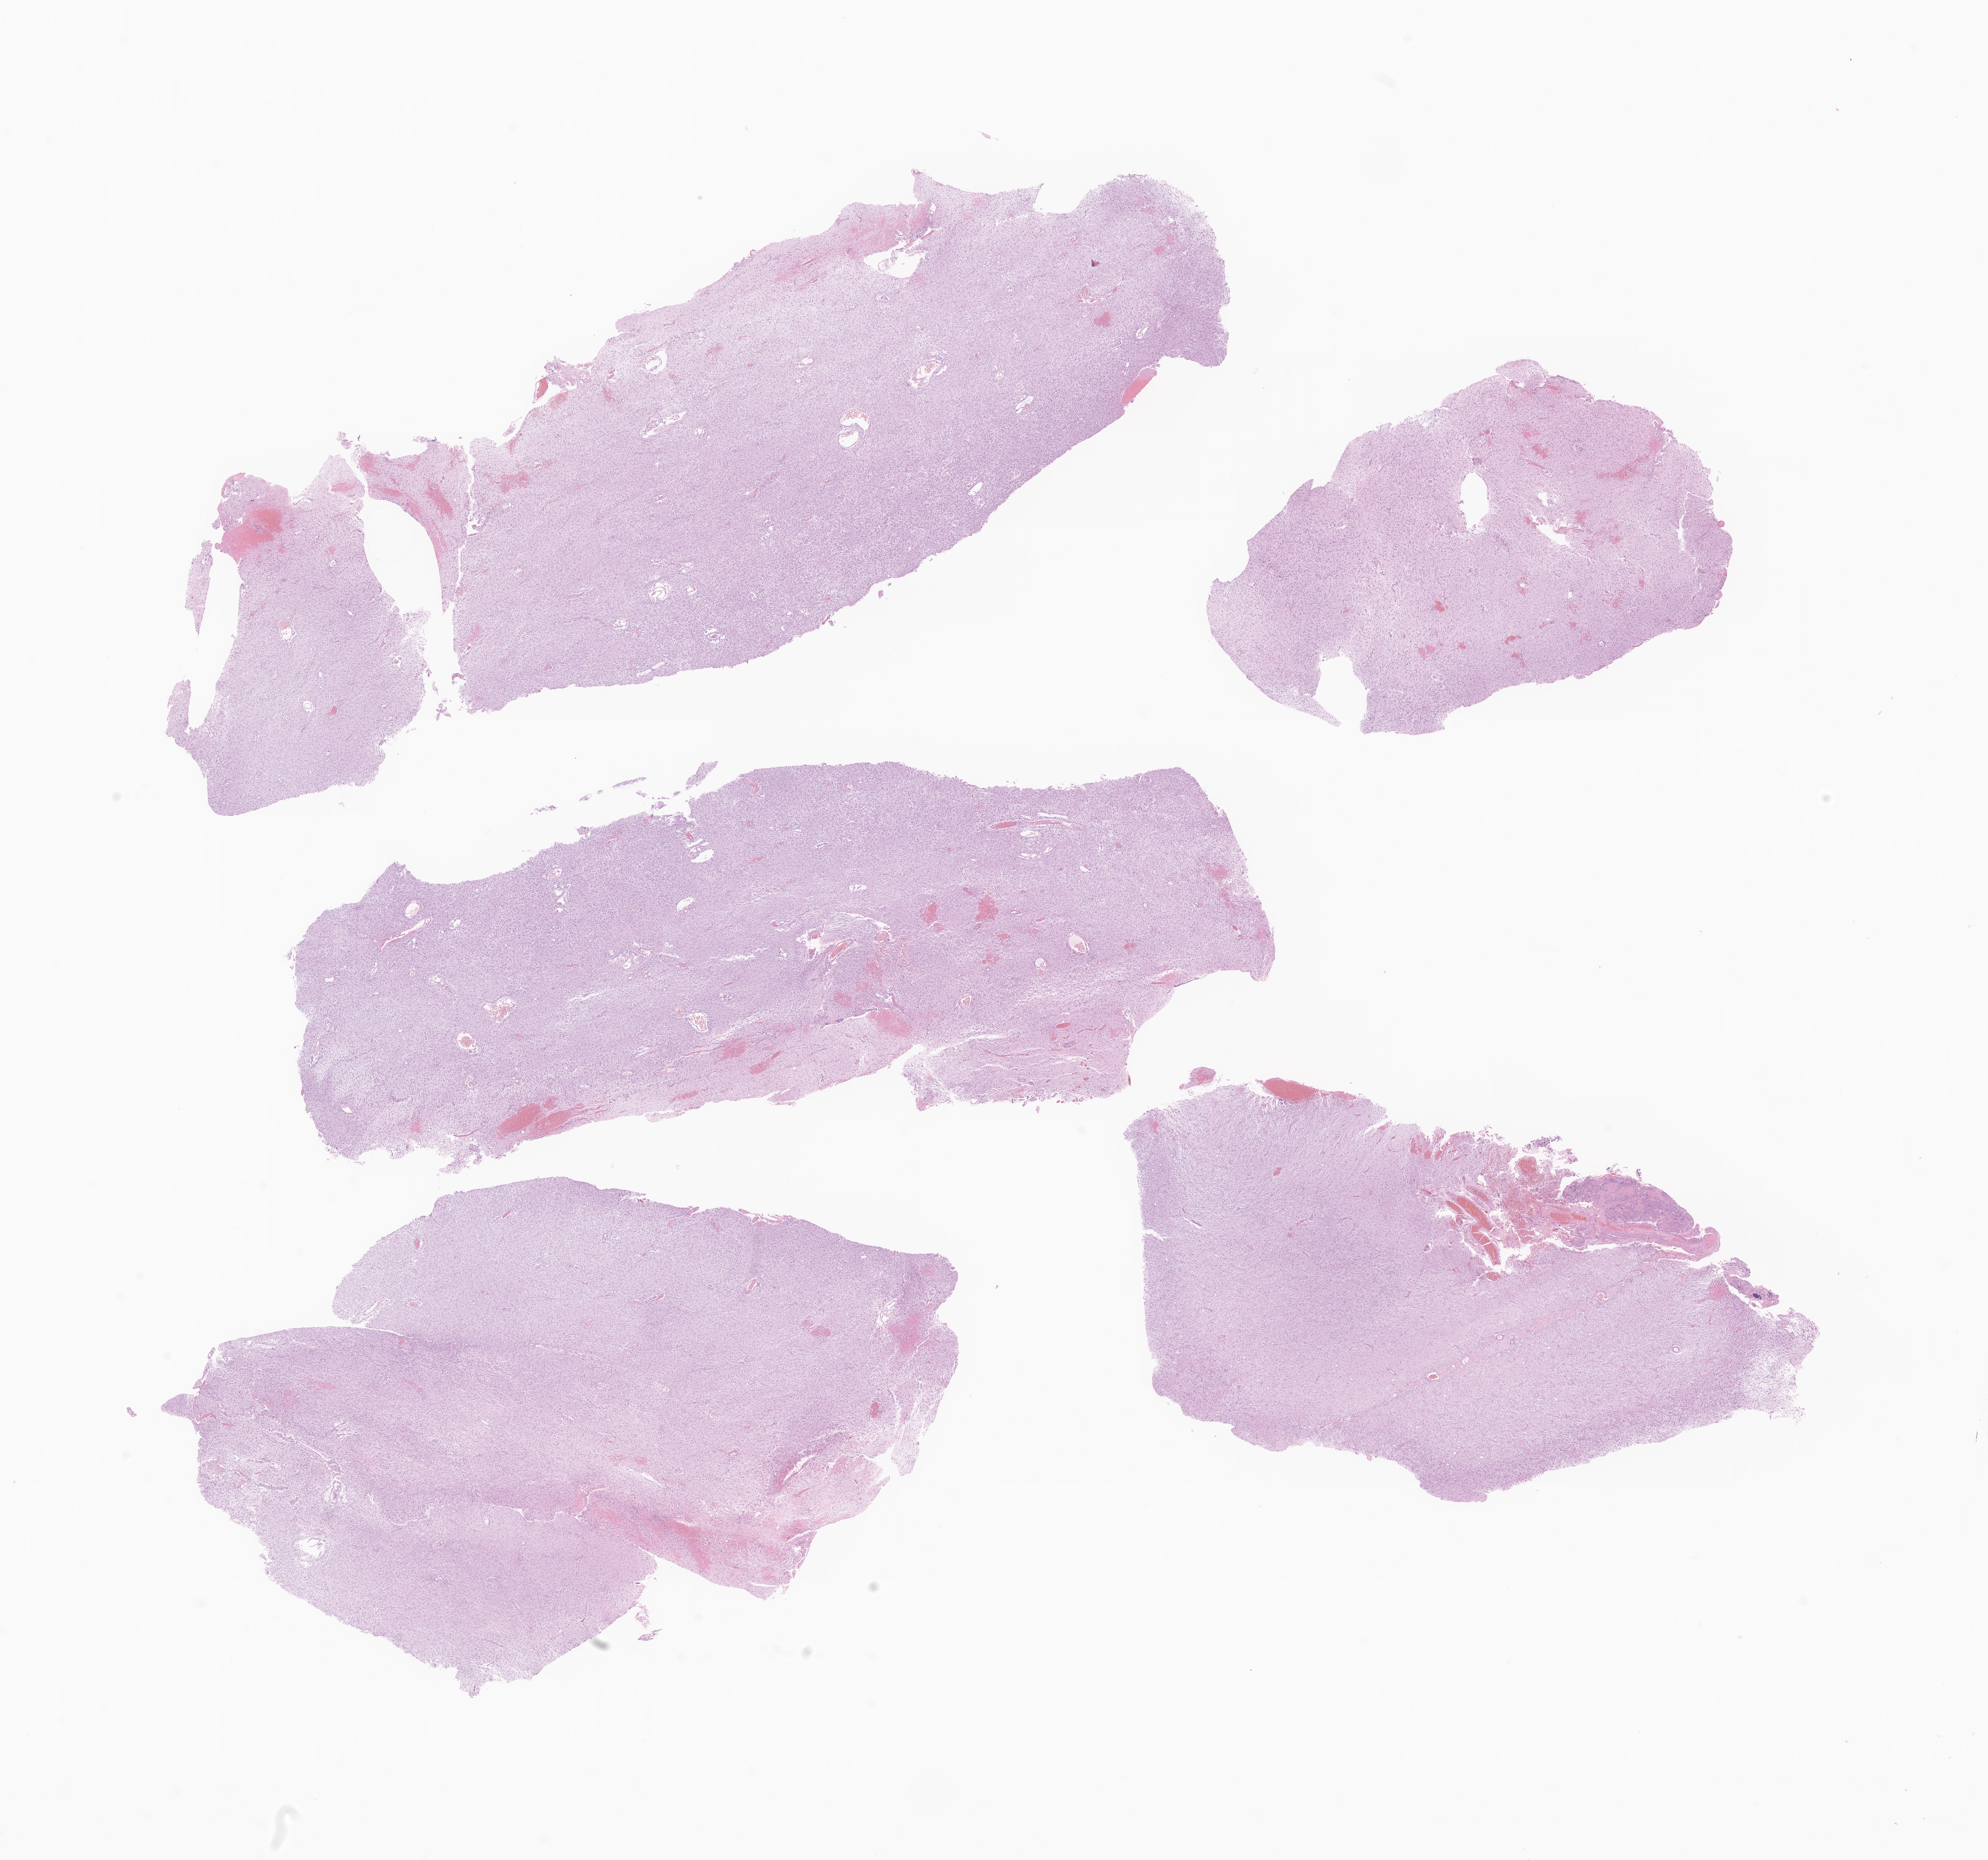
Whole-slide image, H&E stain of tumor tissue from the brain, a low-resolution overview of the entire scanned area, about 22.2 x 20.8 mm; formalin-fixed paraffin-embedded section. Patient: female, age 53 months.
Recorded diagnosis: Pilocytic astrocytoma.